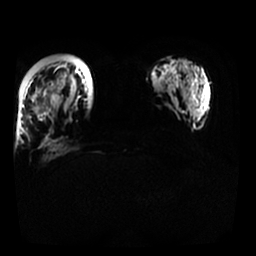
Breast MRI, one axial slice. Position 8 of 25 along the scan axis. Diffusion-weighted series; image 2 of 4 stored at this slice position (different b-values; order by instance number). 1.5 T. 4 mm slice thickness. 256 × 256 image matrix, field of view 340 × 340 mm. Female patient.
Annotated regions visible in this slice (outlined manually by an expert reader):
- tumour on diffusion-weighted imaging: bounding box <41,84,57,113> (left, top, right, bottom; pixels)